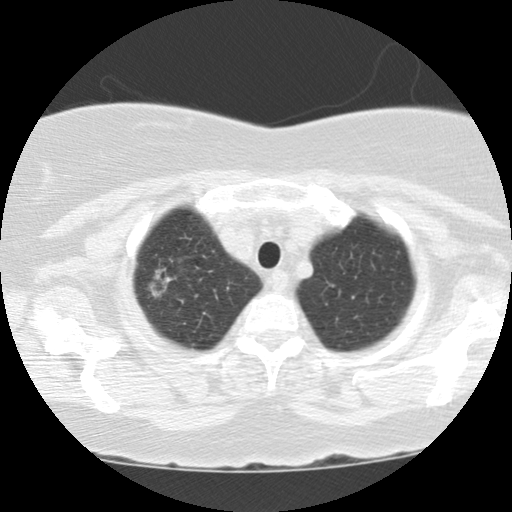
Chest CT (low-dose screening protocol), one axial image. First (baseline) screen. Lung window (W 1500 / L -600 HU). 2.5 mm slice thickness. Standard (soft-tissue) reconstruction kernel (STANDARD). Slice 12 of 112 in the series. 512 × 512 image matrix, field of view 310 × 310 mm. Female participant, aged 67 years at enrolment. Former smoker at enrolment.
- Expert reader's lesion annotation, bounding box <131,247,198,309> (left, top, right, bottom; pixels).
- The screening reader recorded 3 non-calcified nodules or masses ≥4 mm on this exam (right upper lobe, right lower lobe, right upper lobe); which of them this box marks is not recorded.
- Later outcome: lung cancer diagnosed 441 days after this screen — adenocarcinoma with mixed subtypes, right upper lobe, poorly differentiated (G3), stage IA (AJCC 6th edition), 30 mm at pathology.